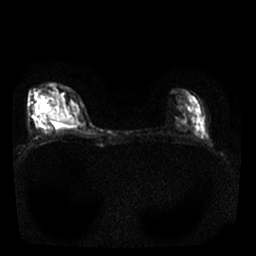
Breast MRI, one axial slice; position 13 of 25 along the scan axis; diffusion-weighted series; image 2 of 4 stored at this slice position (different b-values; order by instance number); 1.5 T; 4 mm slice thickness; 256 × 256 image matrix. Female patient.
Annotated regions visible in this slice (expert manual segmentation):
- tumour on diffusion-weighted imaging: bounding box (x1, y1, x2, y2) in pixels: (40, 110, 78, 125)